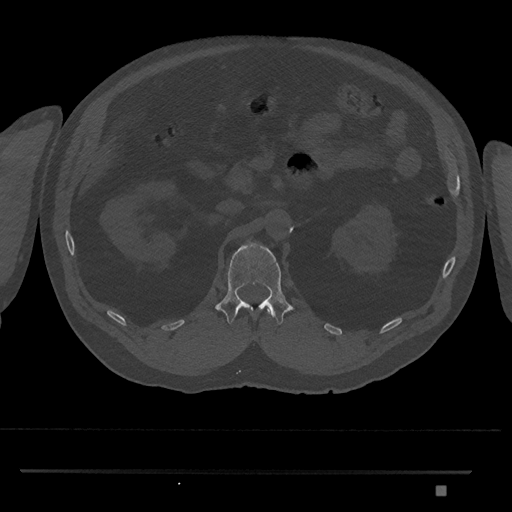
CT including the spine, one axial slice; position 831 of 1134 along the scan axis; bone window (W 1800 / L 400 HU); 0.5 mm slice thickness; 512 × 512 image matrix, field of view 429 × 429 mm. Patient: male, 65 years. From the clinical record (not read from this slice): primary cancer: prostate.
Outlined on this slice (semi-automatic segmentation, software-assisted and operator-edited):
- L1 vertebra: bounding box <215,242,294,325> (left, top, right, bottom; pixels)
- T12 vertebra: <267,310,272,315>